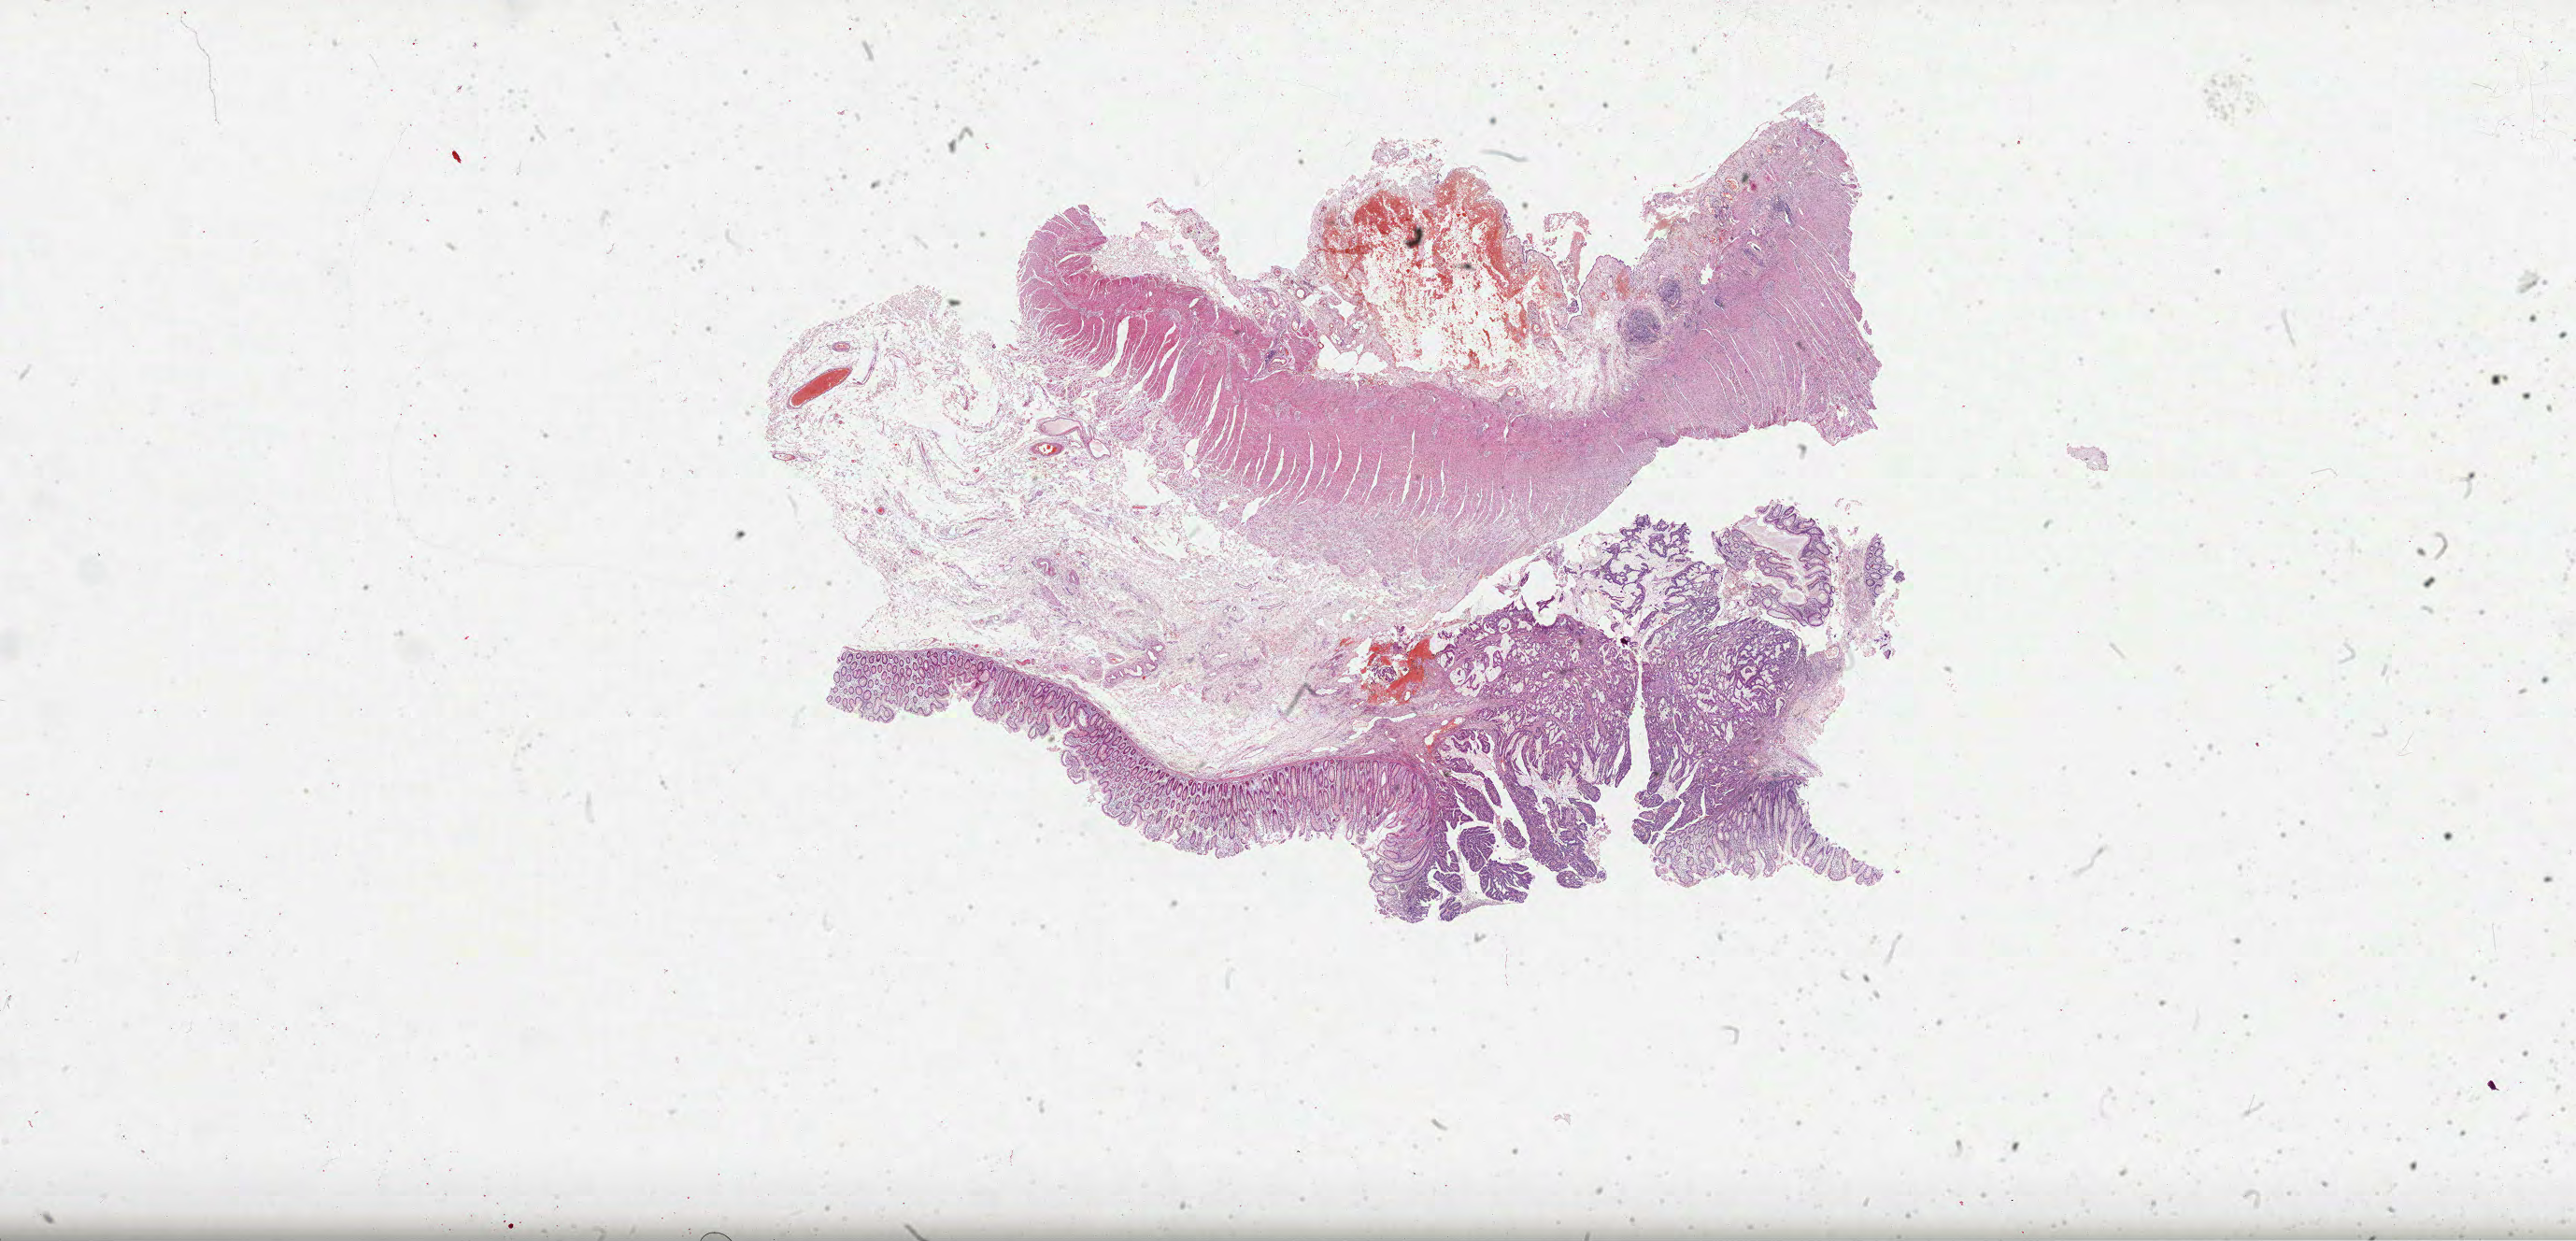
Whole-slide histology image, Hematoxylin and eosin (H&E) stained, whole scanned area (about 44.5 x 21.4 mm) shown as a low-resolution overview. Formalin-fixed paraffin-embedded (FFPE) diagnostic section. Colon, primary tumour sample. Patient: male, age at initial diagnosis 66 years.
Lymph nodes positive (case pathology): 0 of 13 examined. Pathologic diagnosis: Mucinous adenocarcinoma (cecum). AJCC pathologic stage: I.